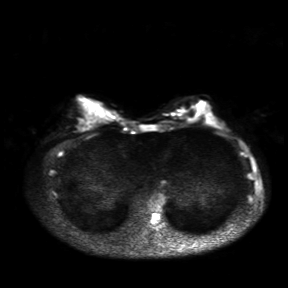
Breast MRI, one axial slice; slice 11 of 30 in the series (ordered by position); diffusion-weighted series; image 2 of 4 stored at this slice position (different b-values; order by instance number); 3 T; 4 mm slice thickness; 288 × 288 image matrix, field of view 360 × 360 mm. Female patient.
Outlined on this slice (outlined manually by an expert reader):
- tumour on diffusion-weighted imaging: bounding box (x1, y1, x2, y2) in pixels: (173, 109, 186, 115)